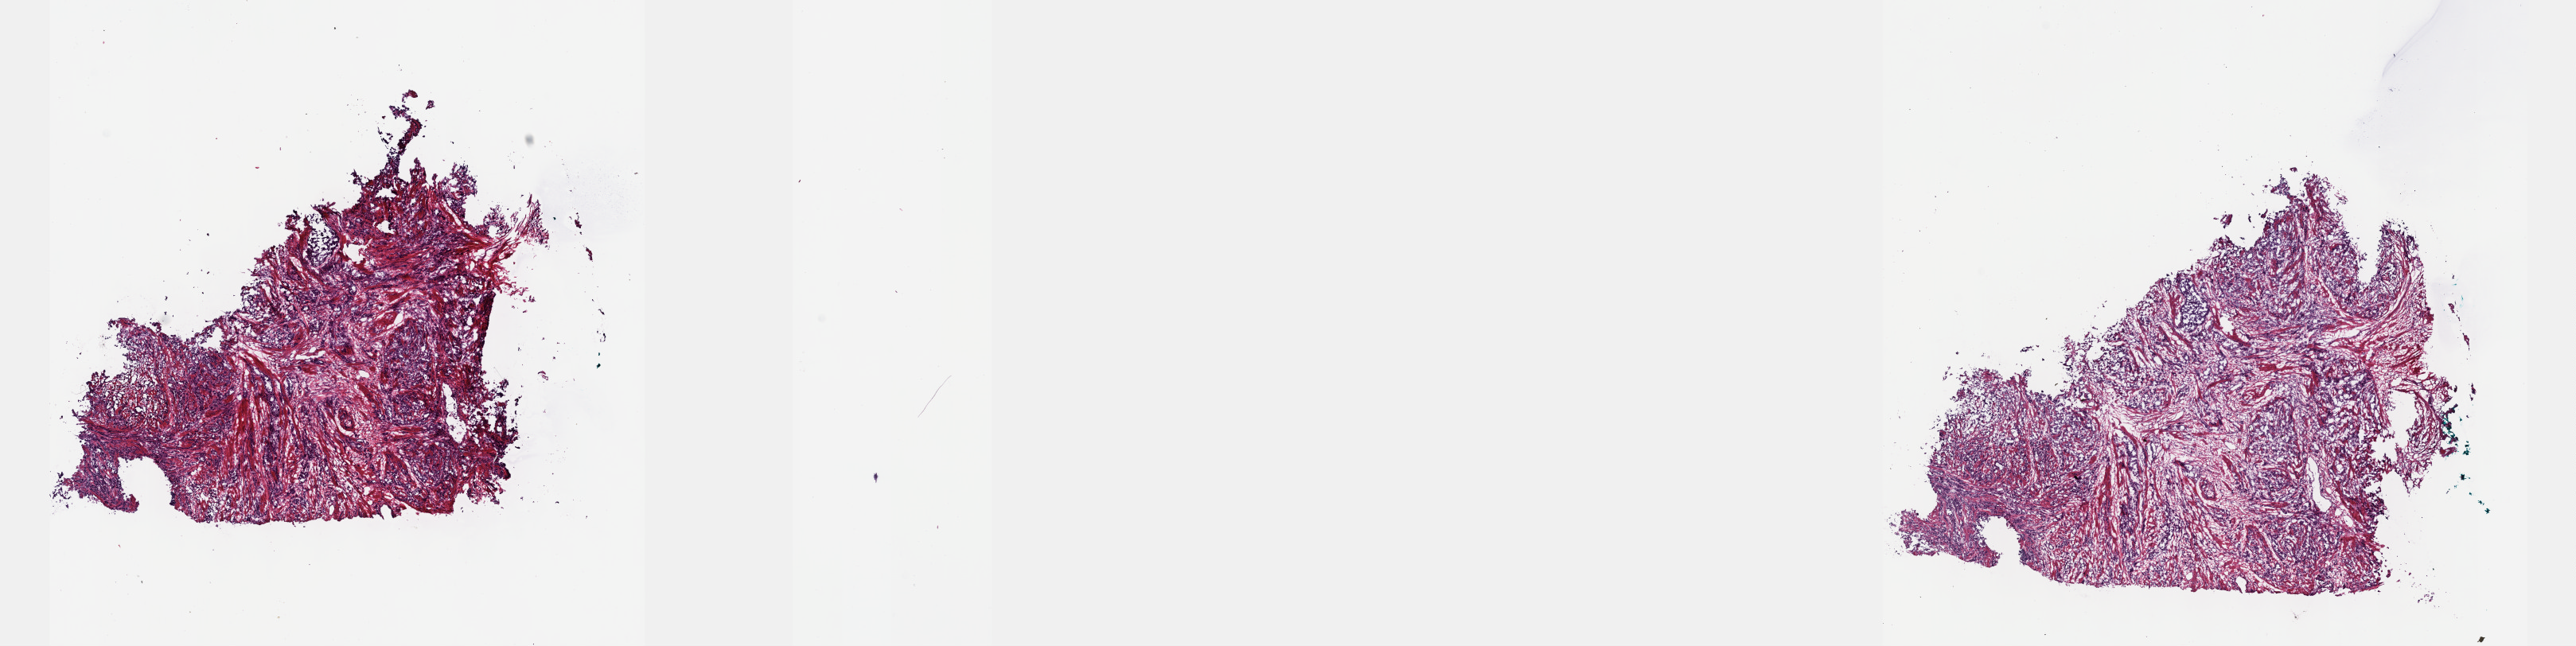
Whole-slide histology image, H&E — a low-resolution overview of the entire scanned area, about 26.2 x 6.6 mm (from a 40x scan). Frozen section from the top of the tissue portion. Prostate, primary tumour sample. Male, age 73 years at initial diagnosis. Gleason score: 9 (5+4). Slide review estimates, as recorded: tumour cells 80%, tumour nuclei 80%, normal cells 0%, stromal cells 19%, necrosis 1%. Inflammatory infiltration, as recorded: lymphocyte infiltration 3%, monocyte infiltration 1%, neutrophil infiltration 1%.
- lymph nodes positive (case pathology): 1 of 30 examined
- diagnosis: Adenocarcinoma, NOS (prostate gland)